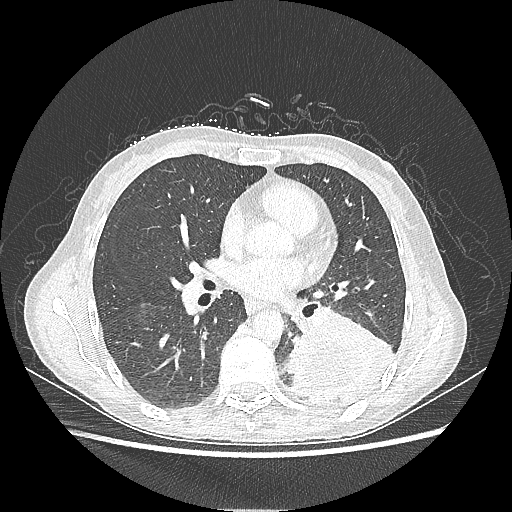
Chest CT, one axial slice. Position 112 of 220 along the scan axis. Reconstruction kernel LUNG. Lung window (W 1500 / L -600 HU). 1.25 mm slice thickness. 512 × 512 image matrix, field of view 360 × 360 mm. Female patient, age 53 years. From the clinical record (not read from this slice): clinical TNM (as recorded): T3 N0 M0.
Structures marked on this image (rectangle marked by the reading radiologist):
- lung tumour (recorded histology: adenocarcinoma): bounding box <284,306,398,414> (left, top, right, bottom; pixels)